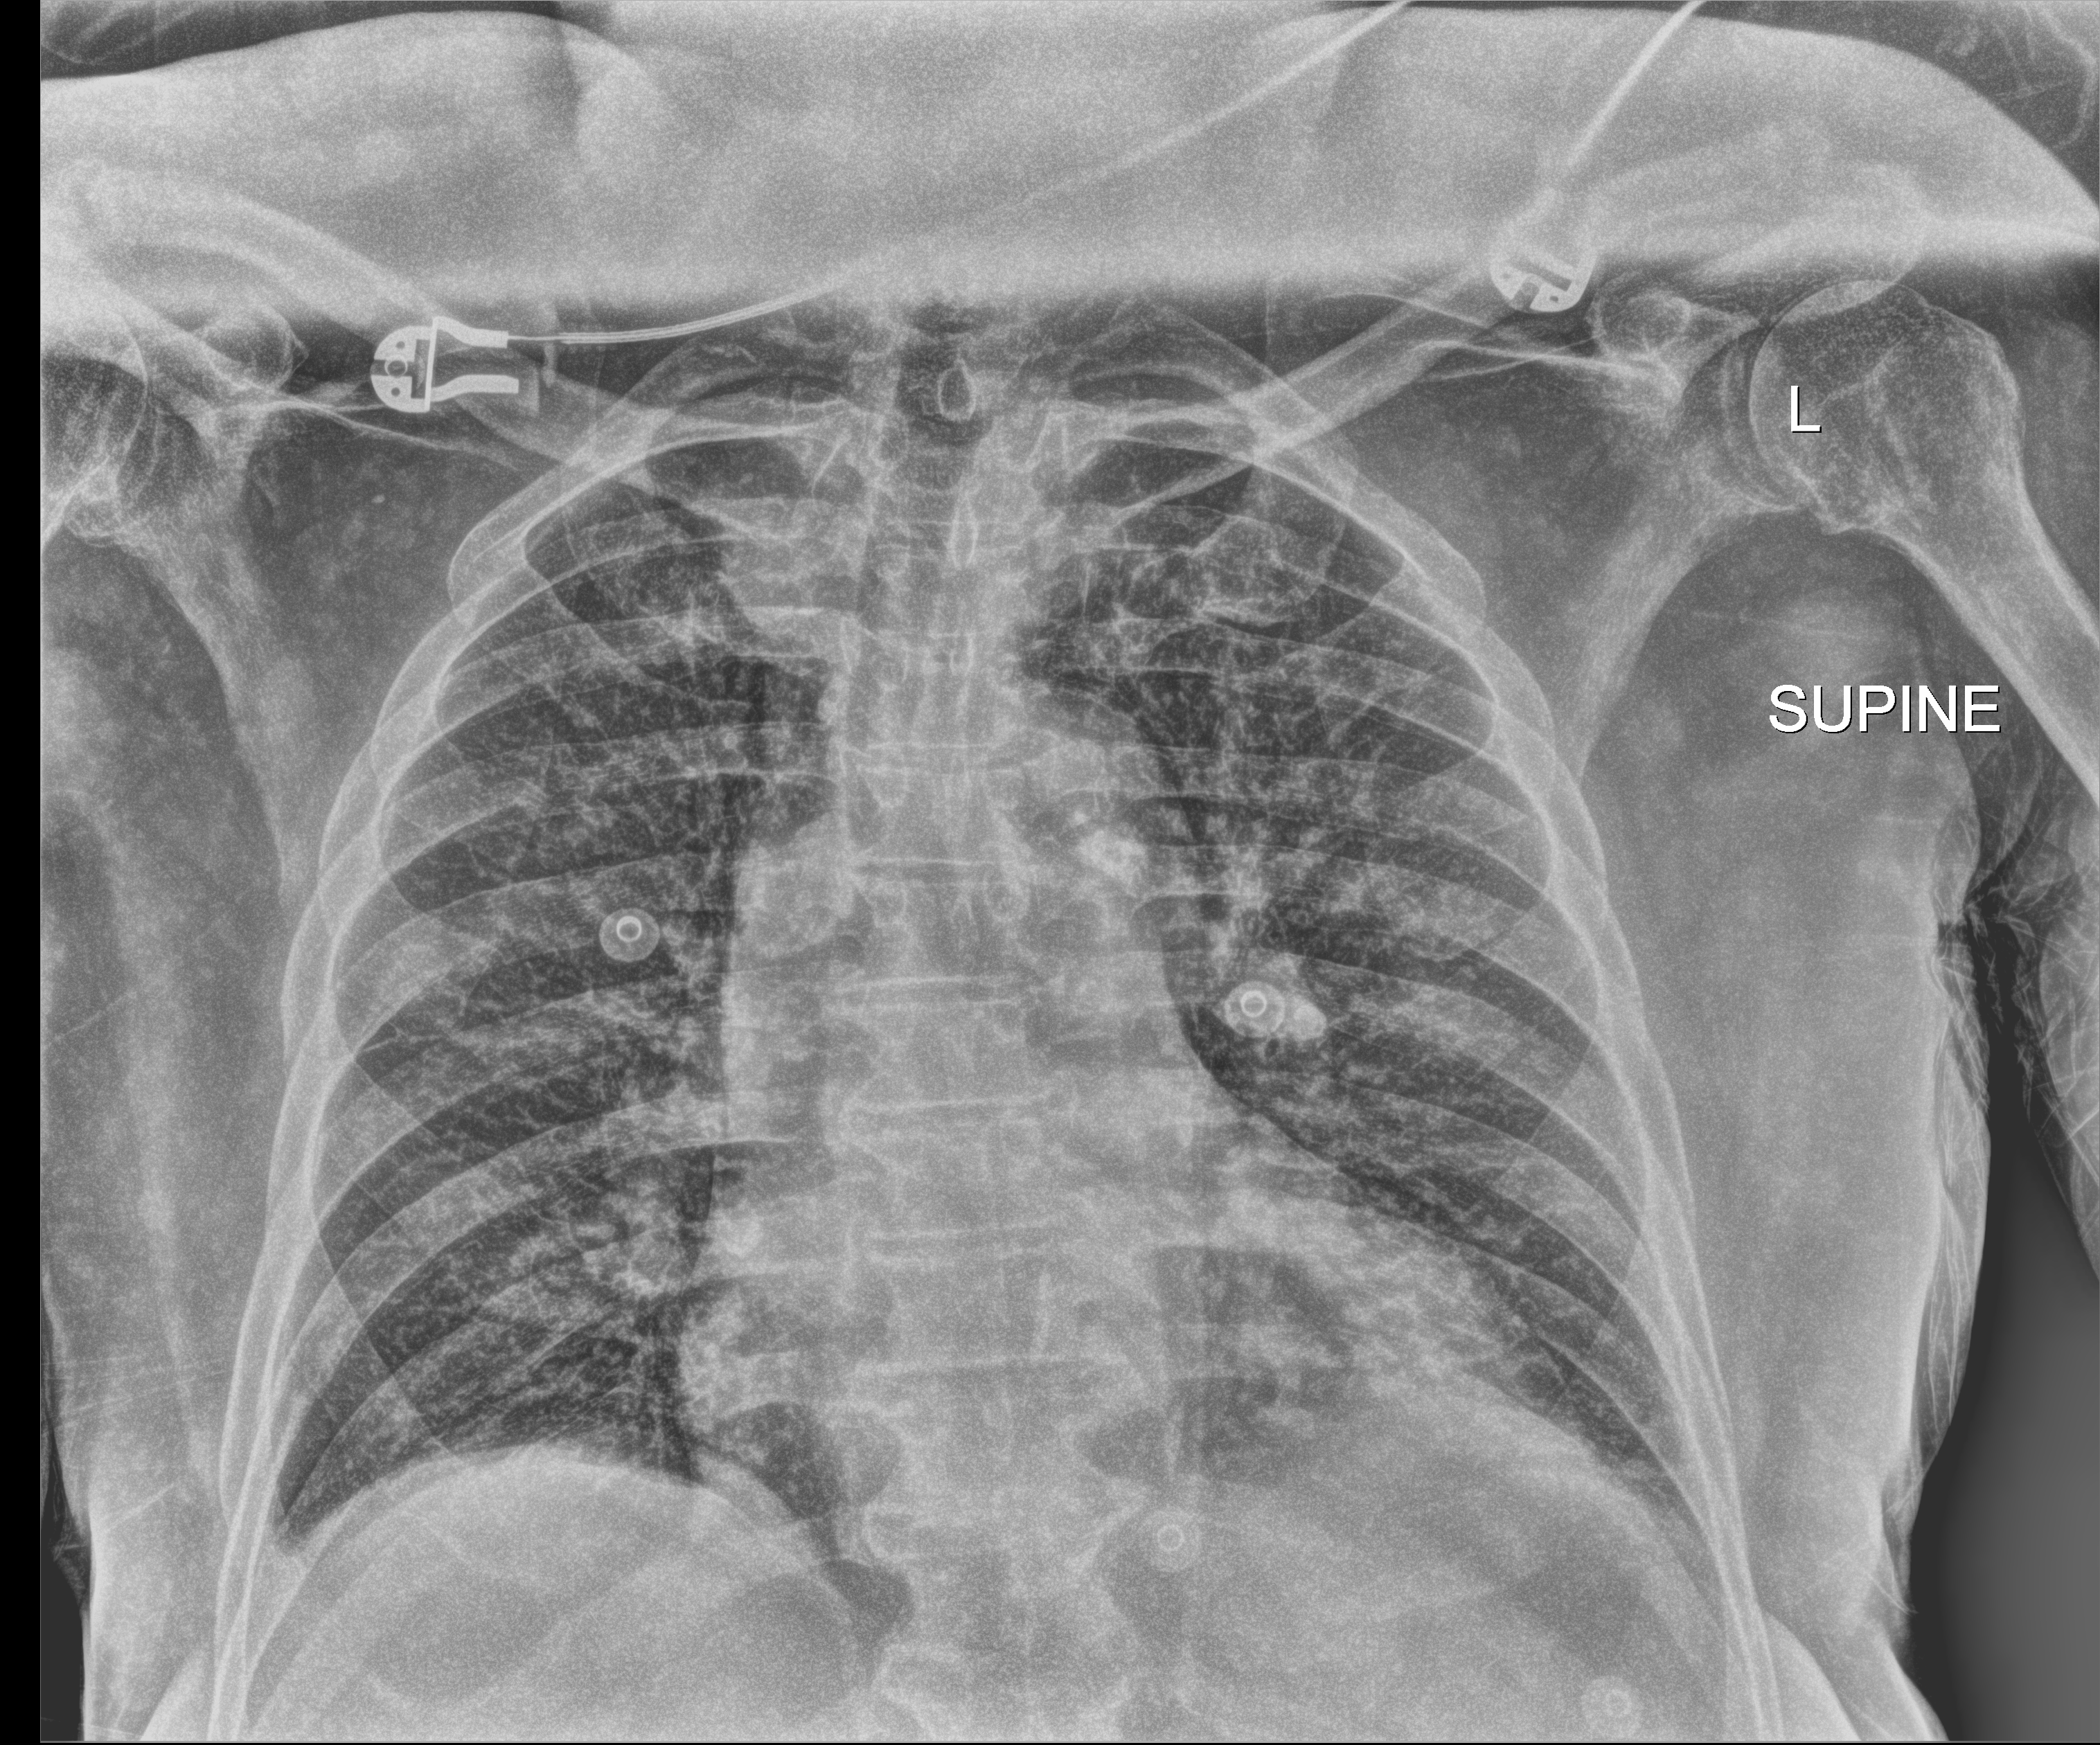
Chest X-ray (portable); anteroposterior (AP) projection. Patient hospitalised with COVID-19; male, aged 75–90 years.
From the hospital-stay record, not from the radiograph (when in the stay this image was taken is not recorded):
- length of hospital stay: 2 days
- admitted to intensive care during this hospital stay: no
- mechanically ventilated during this hospital stay: no